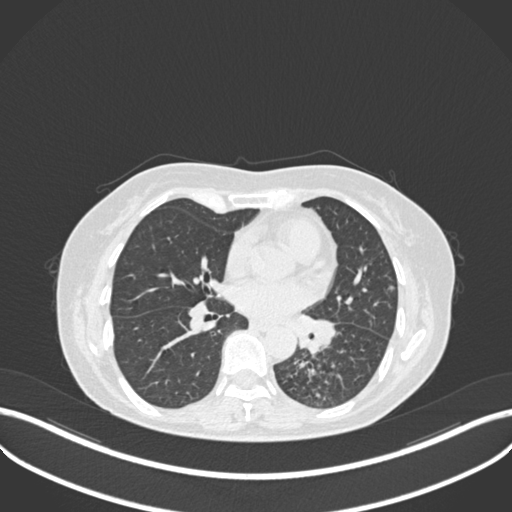
Chest CT, one axial slice. Slice 123 of 270 in the series (ordered by position). Reconstruction kernel B30f. 120 kVp. Lung window (W 1500 / L -600 HU). 512 × 512 image matrix, field of view 400 × 400 mm. Patient: female, 63 years. From the clinical record (not read from this slice): clinical TNM (as recorded): T1b N0 M0.
Outlined on this slice (bounding box drawn by a radiologist):
- lung tumour (recorded histology: adenocarcinoma): bounding box <291,308,342,359> (left, top, right, bottom; pixels)